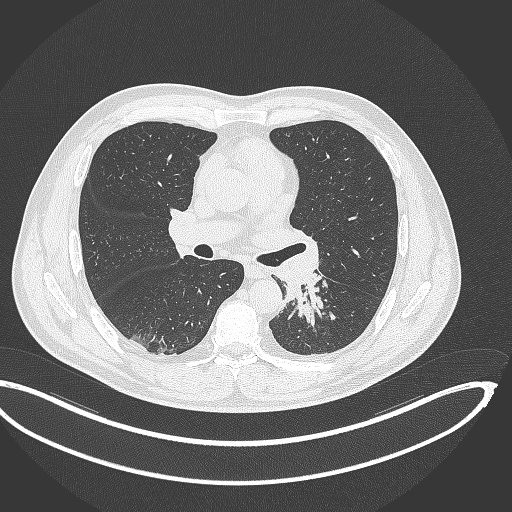
Chest CT, one axial slice; slice 201 of 362 in the series (ordered by position); reconstruction kernel B70f; 120 kVp; lung window (W 1500 / L -600 HU); 512 × 512 image matrix. Patient: male, 50 years. From the clinical record (not read from this slice): clinical TNM (as recorded): T2a N3 M0.
Structures marked on this image (bounding box drawn by a radiologist):
- lung tumour (recorded histology: squamous cell carcinoma): bounding box [x1, y1, x2, y2] px = [279, 268, 330, 326]